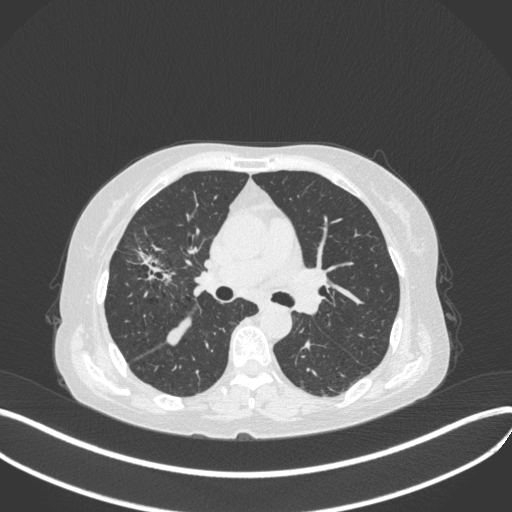
Chest CT, one axial slice. Position 236 of 429 along the scan axis. Reconstruction kernel B31f. Lung window (W 1500 / L -600 HU). 512 × 512 image matrix, field of view 400 × 400 mm. Female patient, age 69 years. Case-level facts recorded for this patient, not image findings: clinical TNM (as recorded): T1b N3 M0.
Structures marked on this image (rectangle marked by the reading radiologist):
- lung tumour (recorded histology: small cell carcinoma): bounding box [x1, y1, x2, y2] px = [126, 241, 183, 298]